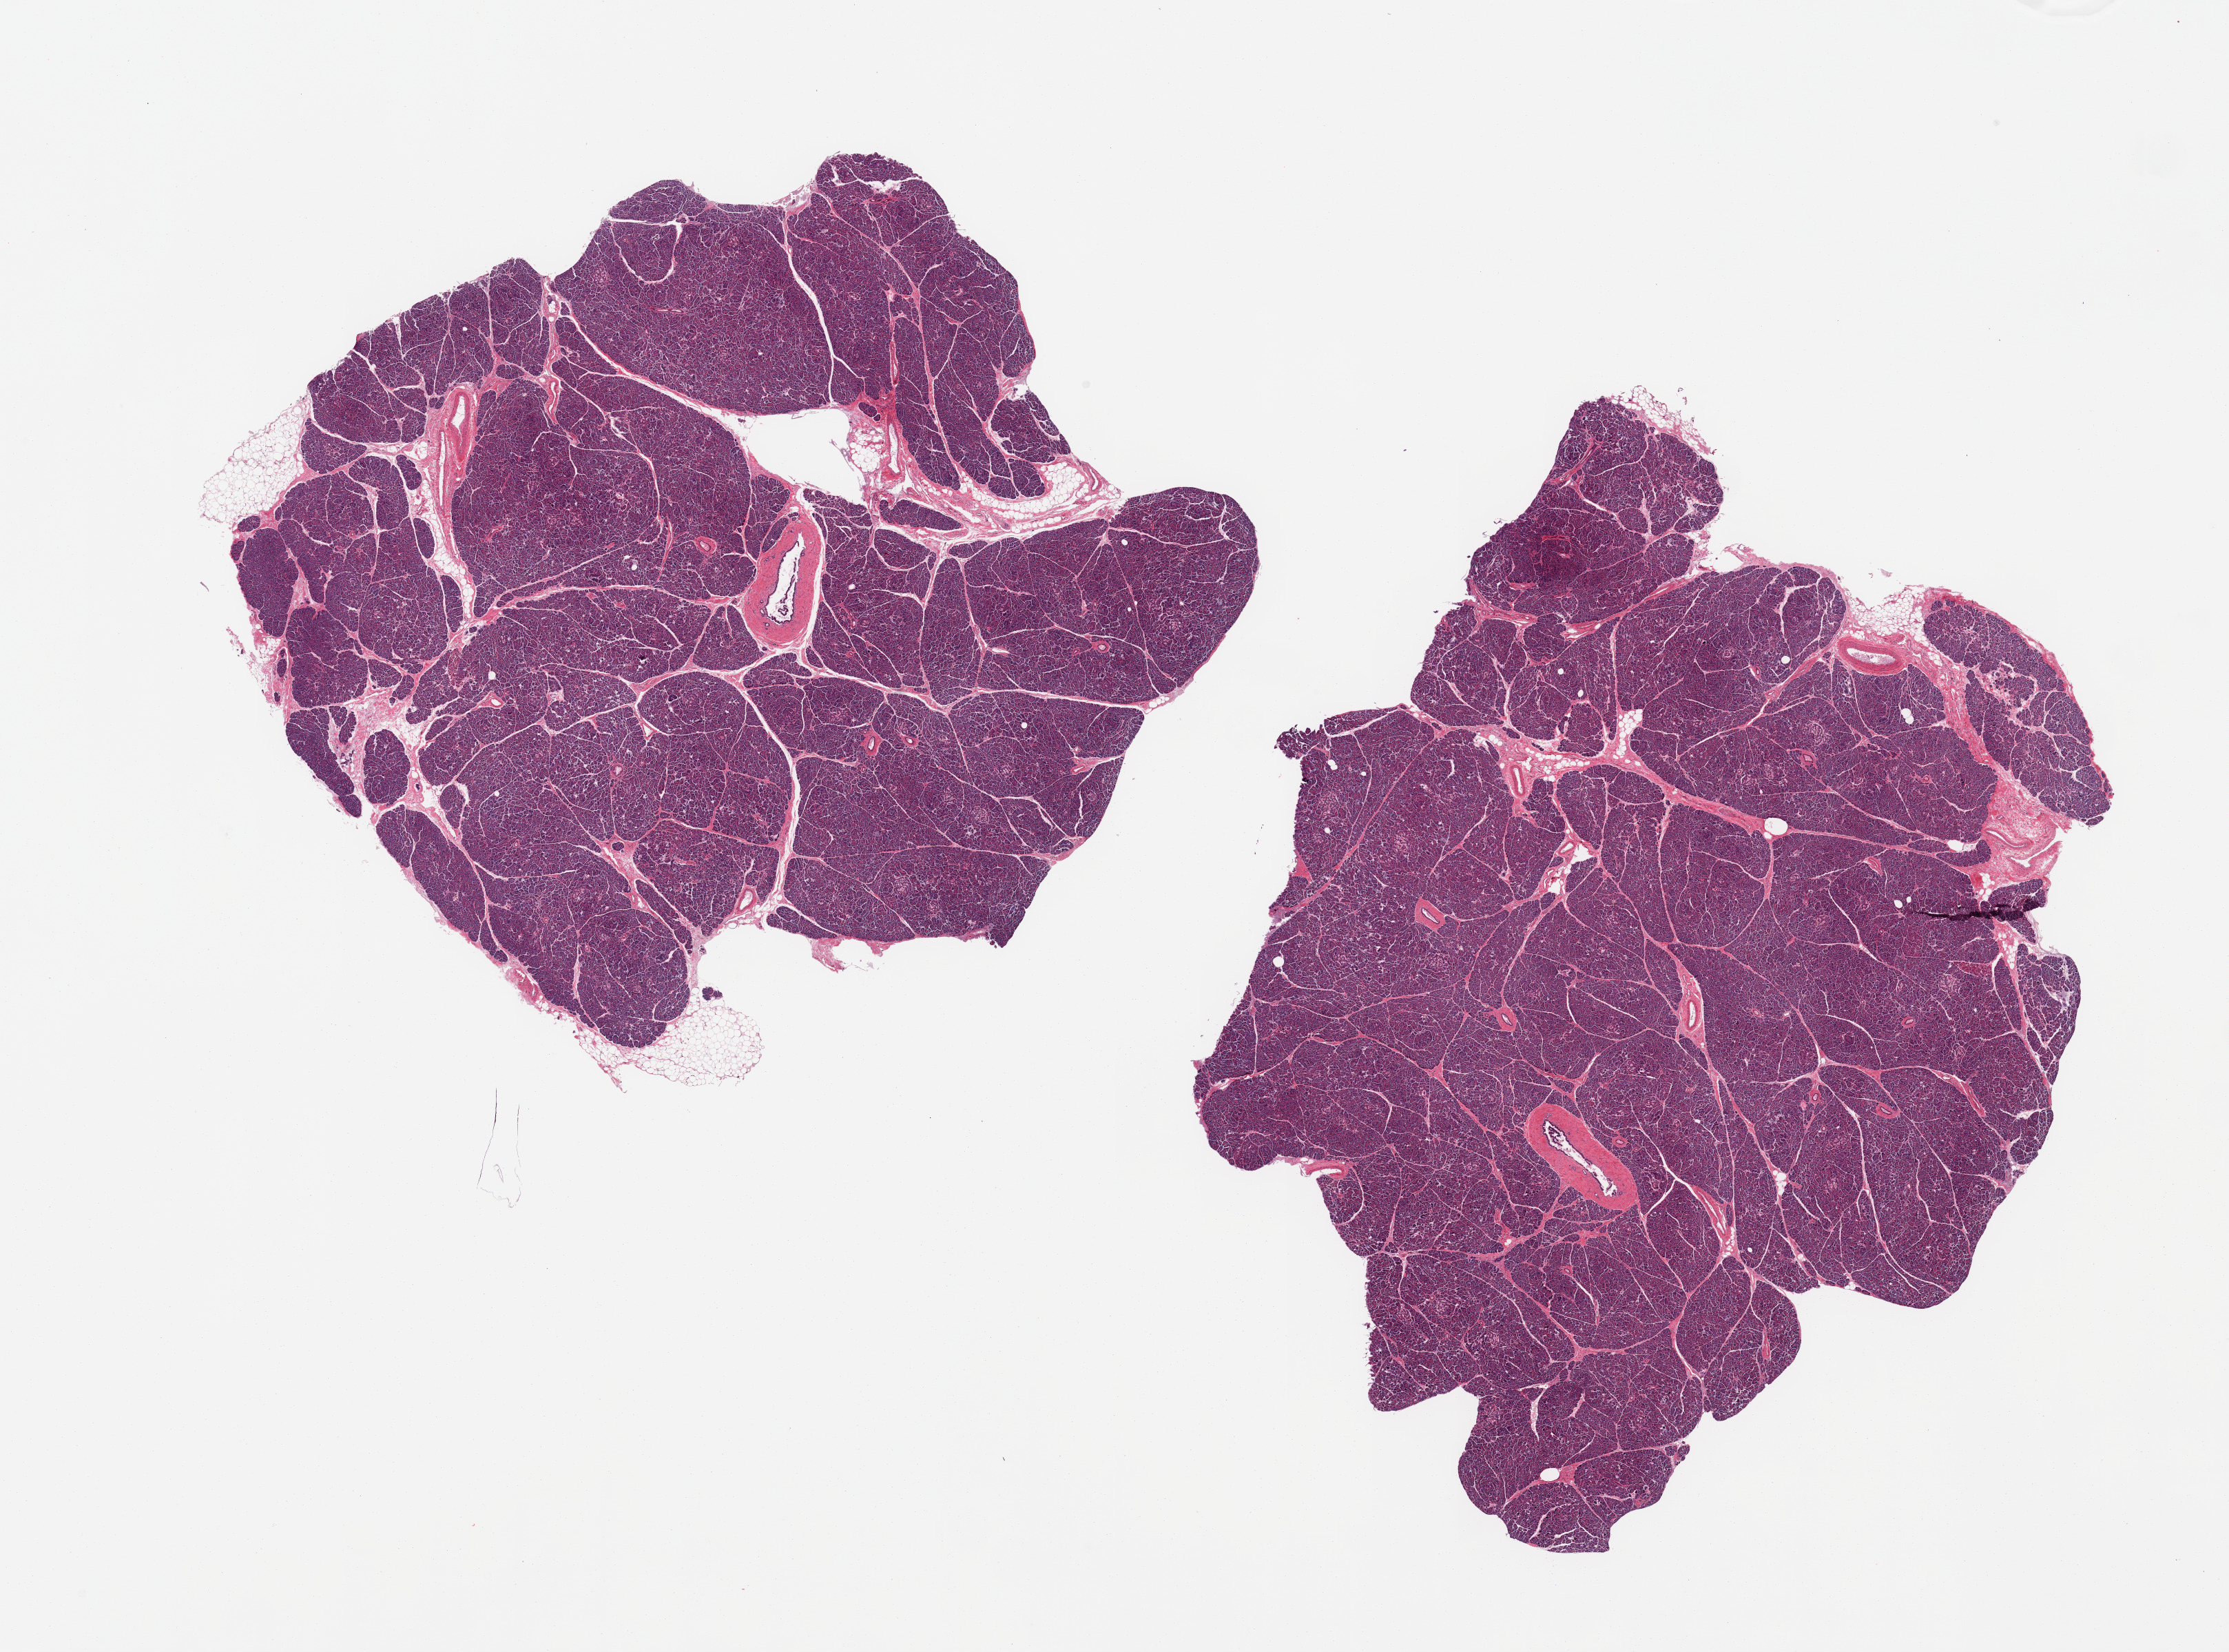
Whole-slide image, H&E stain, a low-resolution overview of the entire scanned area, about 25.6 x 19.0 mm. PAXgene-fixed paraffin-embedded (PFPE) section. Sampled site (target tissue): pancreas. Tissue donor sample. Donor sex: male.
• pathologist's review note for this sample: 2 pieces; minimal attached fat